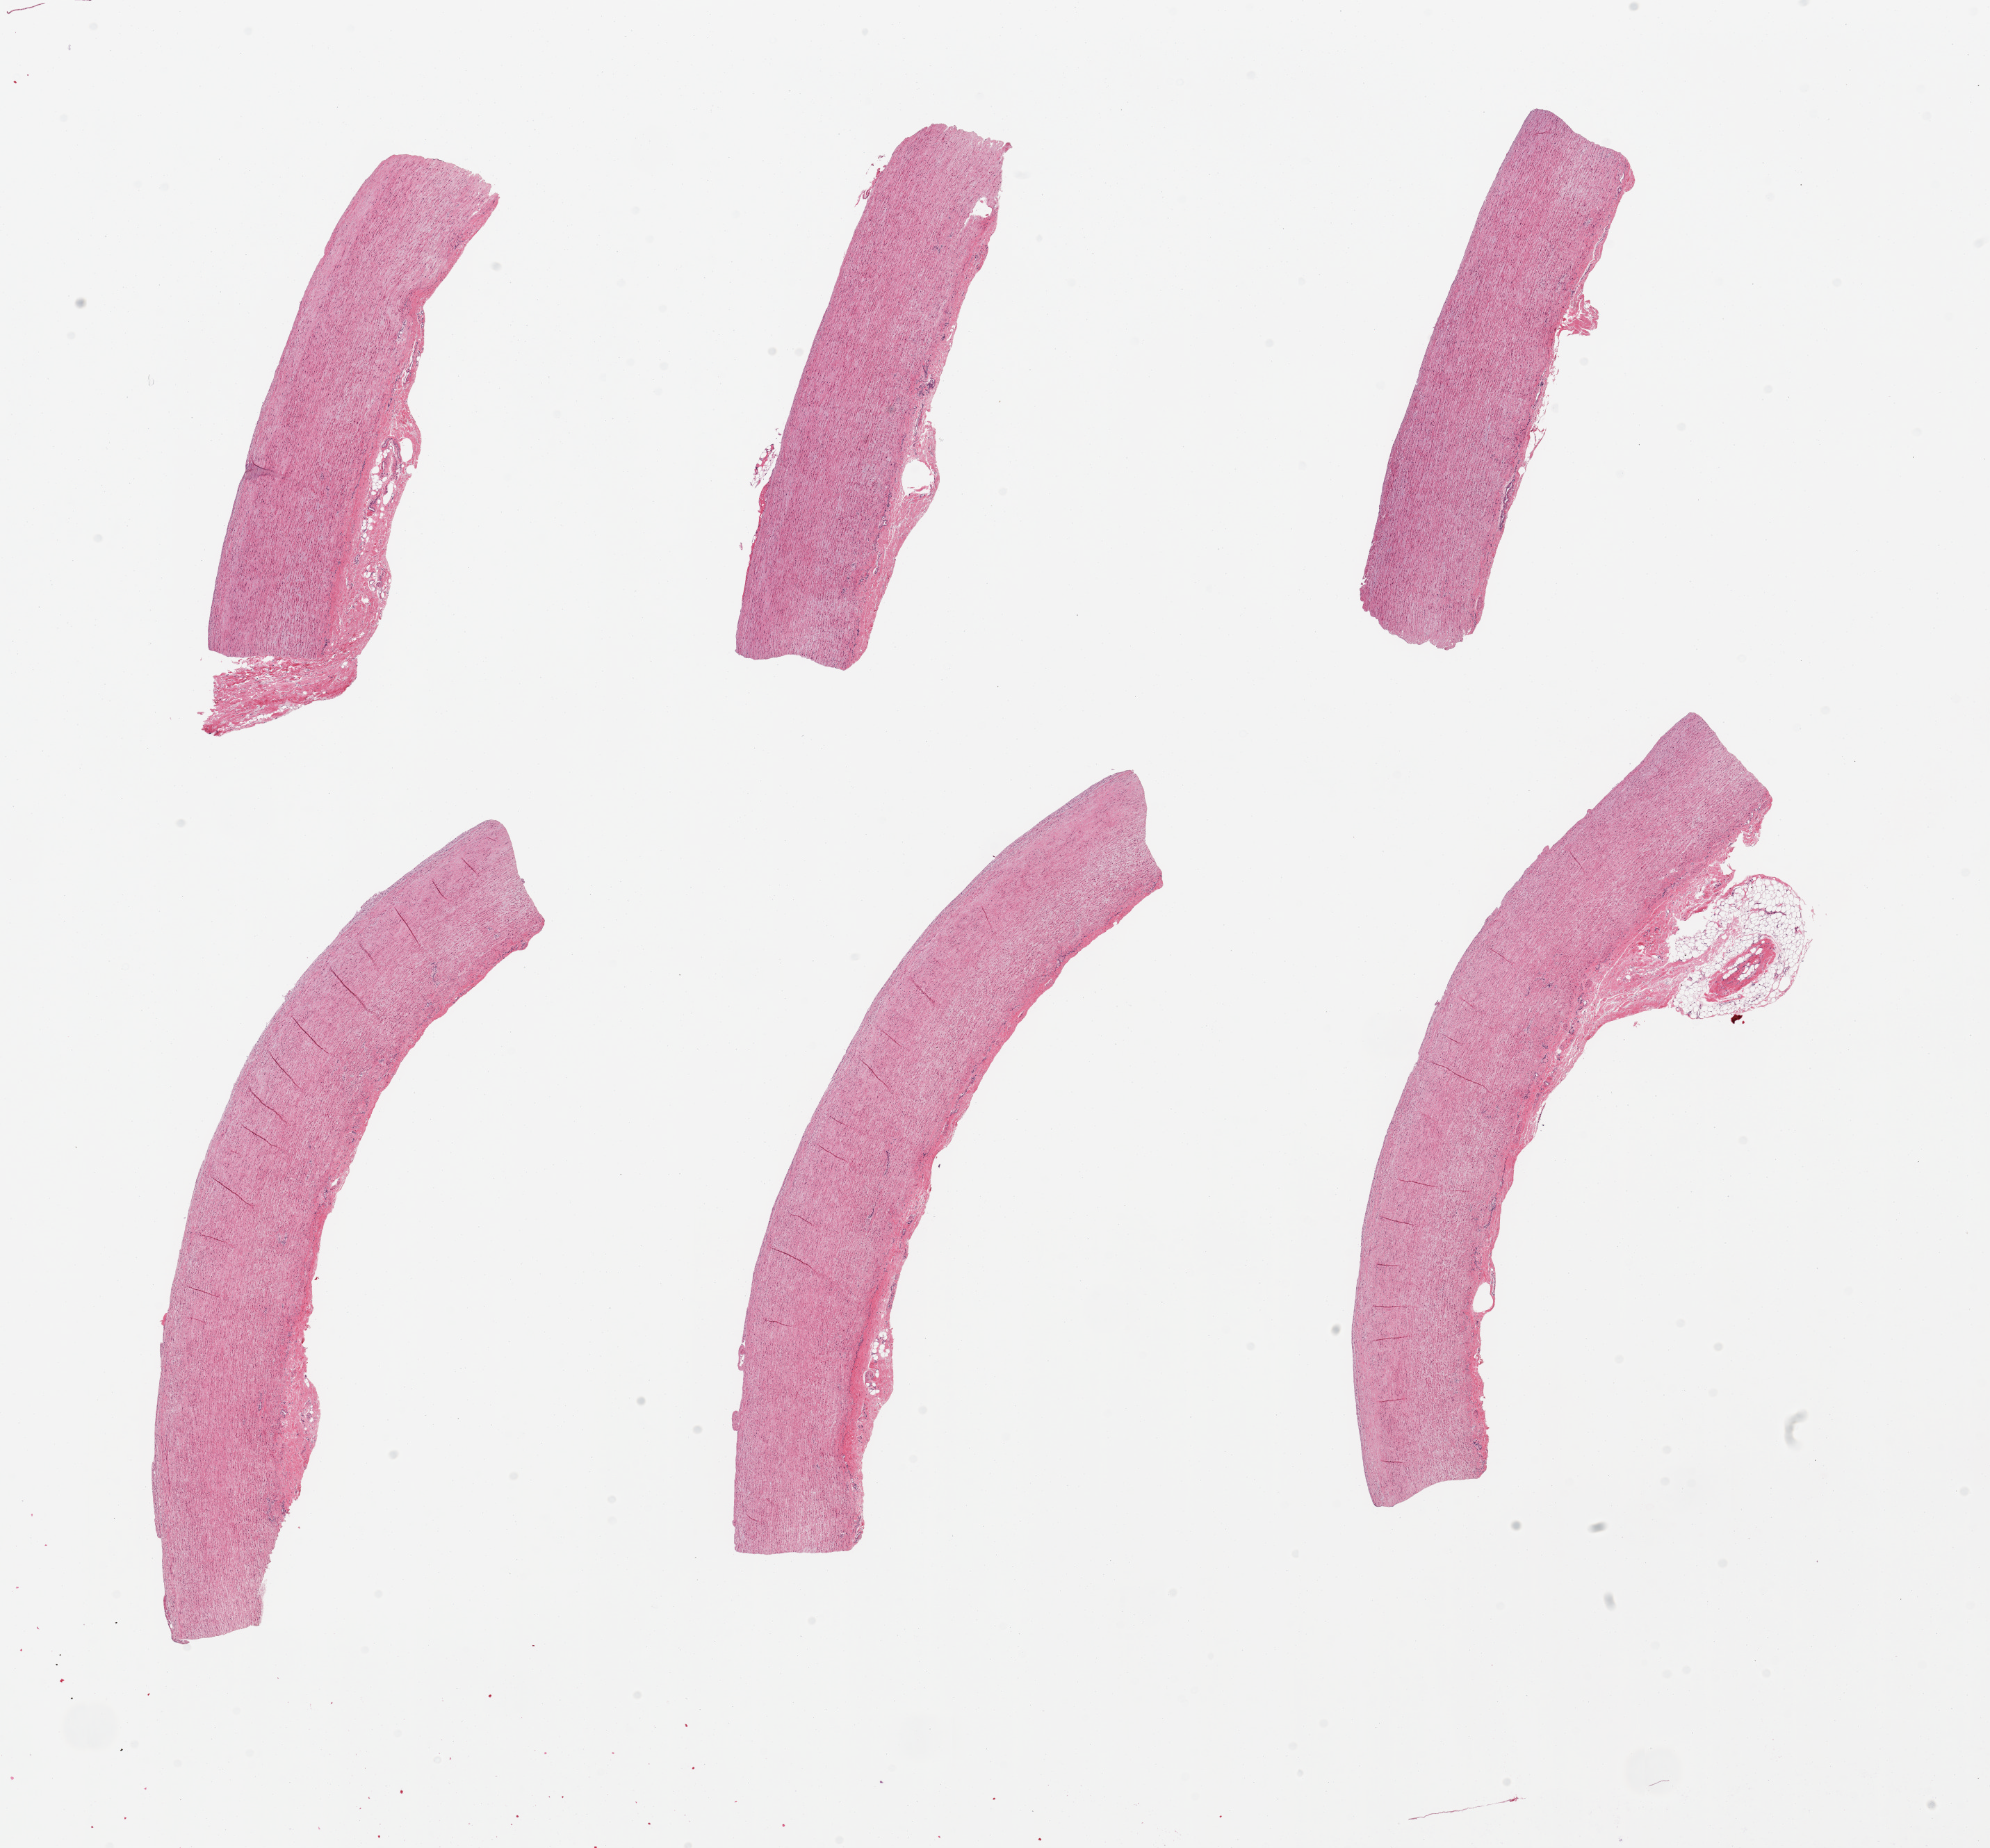
Whole-slide image, hematoxylin and eosin (H&E) stain, shown as a low-resolution overview of the whole scanned area (about 22.6 x 21.0 mm, from a 20x scan); PAXgene-fixed, paraffin-embedded tissue; section of aorta (target tissue); donor tissue sample. Donor: male.
Review note (as recorded): 6 pieces, minimal atherosis.